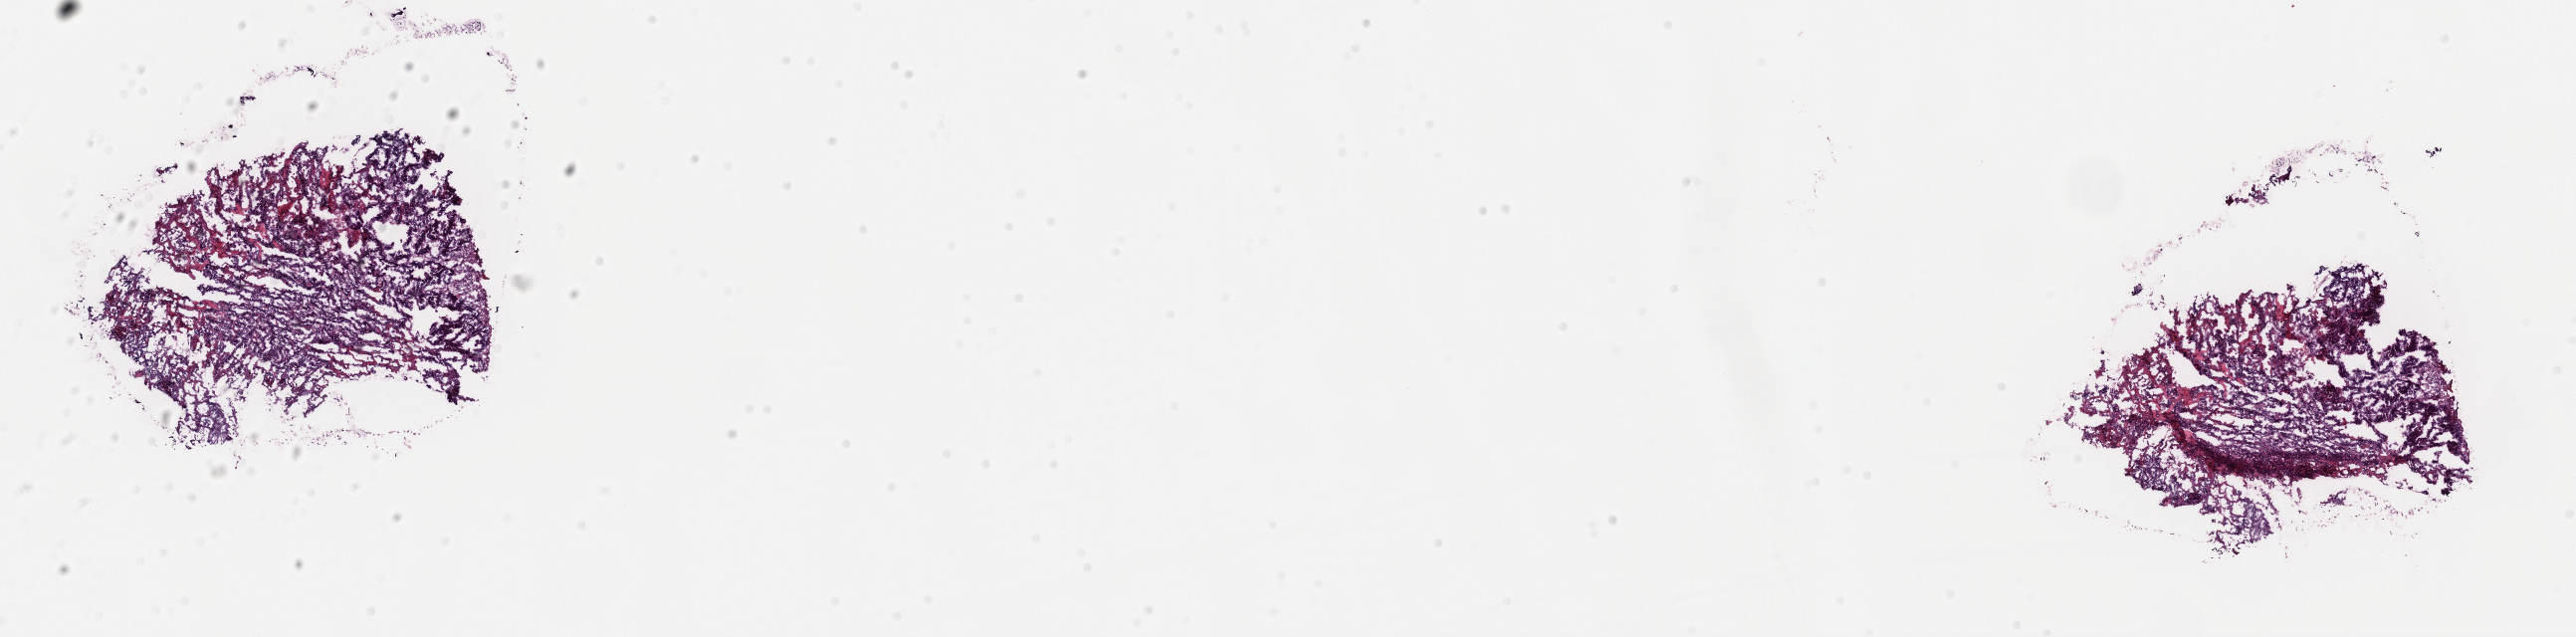
H&E-stained whole-slide image, whole scanned area (about 20.4 x 5.1 mm, from a 40x scan) shown as a low-resolution overview. Frozen section from the top of the tissue portion. Primary tumour sample from the cervix. Patient: female, age at initial diagnosis 65 years. Histologic grade: G2 (moderately differentiated). Slide review estimates, as recorded: tumour cells 85%, tumour nuclei 97%, normal cells 0%, stromal cells 10%, necrosis 5%. Infiltration values recorded for this section: lymphocyte infiltration 1%, monocyte infiltration 0%, neutrophil infiltration 0%.
* FIGO stage: IIA
* diagnosis: Adenocarcinoma, endocervical type (cervix uteri)